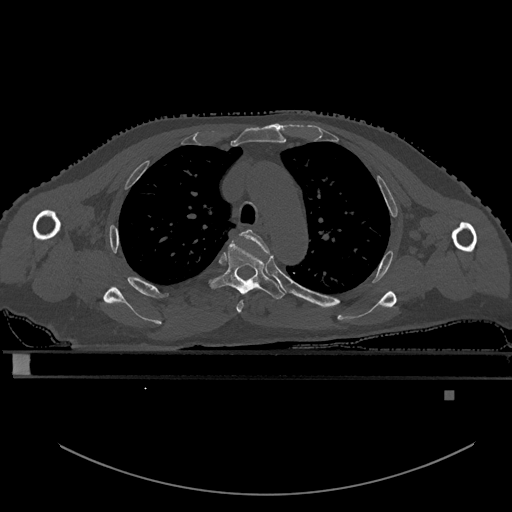
CT including the spine, one axial slice. Position 416 of 969 along the scan axis. Bone window (W 1800 / L 400 HU). 0.5 mm slice thickness. 512 × 512 image matrix, field of view 456 × 456 mm. Patient: male, 82 years. From the clinical record (not read from this slice): primary cancer: prostate; vertebrae with lytic lesions (as recorded): T11, T9, T8, T2.
Structures marked on this image (semi-automatic segmentation, software-assisted and operator-edited):
- T3 vertebra: box from (x=236, y=229) to (x=269, y=313) px
- T4 vertebra: (x=210, y=239)–(x=285, y=300)